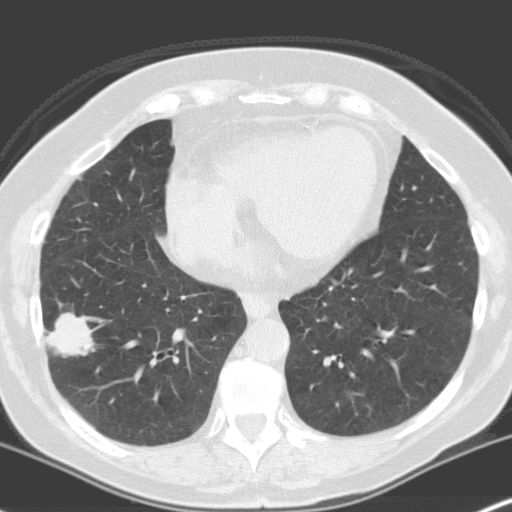
Chest CT (low-dose screening protocol), one axial image; first (baseline) screen; lung window (W 1500 / L -600 HU); 3.2 mm slice thickness; standard (soft-tissue) reconstruction kernel (C); slice 95 of 160 in the series. Female, age 70 years at enrolment. Current smoker at enrolment.
Lesion marked by an expert reader, bounding box [x1, y1, x2, y2] px = [32, 301, 100, 370]. The screening reader recorded 4 non-calcified nodules or masses ≥4 mm on this exam; which of them this box marks is not recorded. Later outcome: lung cancer diagnosed 28 days after this screen — adenocarcinoma, NOS, right lower lobe, moderately differentiated (G2), stage IV (AJCC 6th edition), 28 mm at pathology.